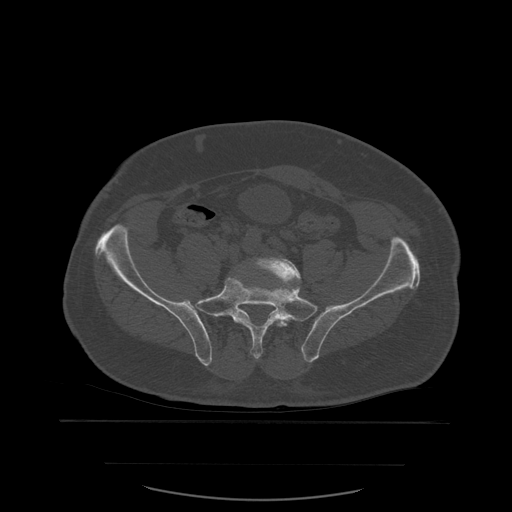
CT including the spine, one axial slice; slice 121 of 590 in the series (ordered by position); bone window (W 1800 / L 400 HU); 1.25 mm slice thickness; 512 × 512 image matrix, field of view 479 × 479 mm. Patient age 71 years. Case-level facts recorded for this patient, not image findings: primary cancer: lung; vertebrae with lytic lesions (as recorded): T1, T2, L5, S1.
Annotated regions visible in this slice (semi-automatically segmented with operator editing):
- L5 vertebra: bounding box [x1, y1, x2, y2] px = [251, 257, 302, 357]